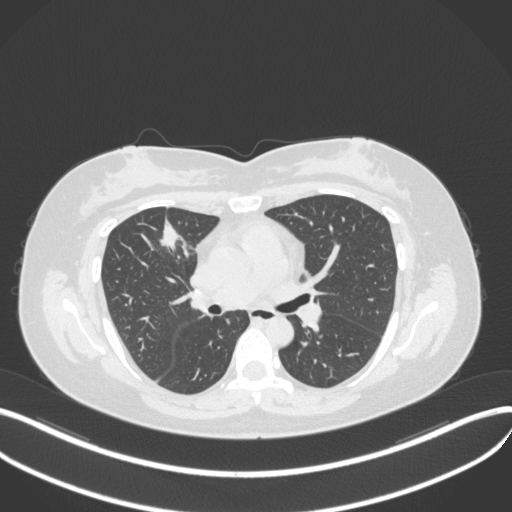
Chest CT, one axial slice; position 183 of 272 along the scan axis; reconstruction kernel B31f; 120 kVp; lung window (W 1500 / L -600 HU); 512 × 512 image matrix, field of view 400 × 400 mm. Patient: female, 42 years. Case-level facts recorded for this patient, not image findings: clinical TNM (as recorded): T1b N0 M0.
Outlined on this slice (bounding box drawn by a radiologist):
- lung tumour (recorded histology: adenocarcinoma): bounding box <153,218,189,253> (left, top, right, bottom; pixels)